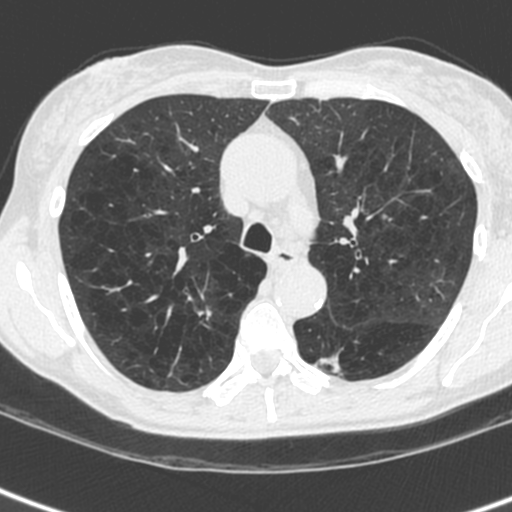
Low-dose screening chest CT, axial slice, first (baseline) screen, lung window (W 1500 / L -600 HU), 1.3 mm slice thickness, 120 kVp, slice 76 of 238 in the series, 512 × 512 image matrix, field of view 282 × 282 mm. Female, age 61 years at enrolment.
Expert-annotated lung lesion, bounding box (x1, y1, x2, y2) in pixels: (181, 298, 225, 338). No non-calcified nodule or mass ≥4 mm was recorded by the screening reader at this exam. Official screen result: negative screen, no significant abnormalities. Lung cancer was diagnosed 836 days after this screen (after the third annual screen): non-small cell carcinoma, right upper lobe, undifferentiated (G4), stage IA (AJCC 6th edition), 15 mm at pathology.